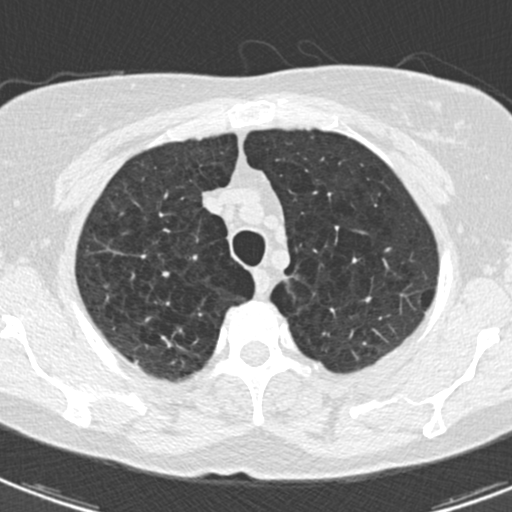
Axial slice from a low-dose chest CT screening exam. Third screening round (two years after baseline). Lung window (W 1500 / L -600 HU). 2 mm slice thickness. Standard (soft-tissue) reconstruction kernel (B30f). Slice 29 of 174 in the series. Female, age 59 years at enrolment. Current smoker at enrolment.
Lesion marked by an expert reader, bounding box <134,320,198,369> (left, top, right, bottom; pixels). The exam's reader record, not a measurement of the box and not confirmed to be the same lesion: non-calcified nodule or mass ≥4 mm, right upper lobe, 12 × 7 mm, spiculated (stellate) margins, soft tissue attenuation, pre-existing on the prior screen: yes; interval growth: yes.